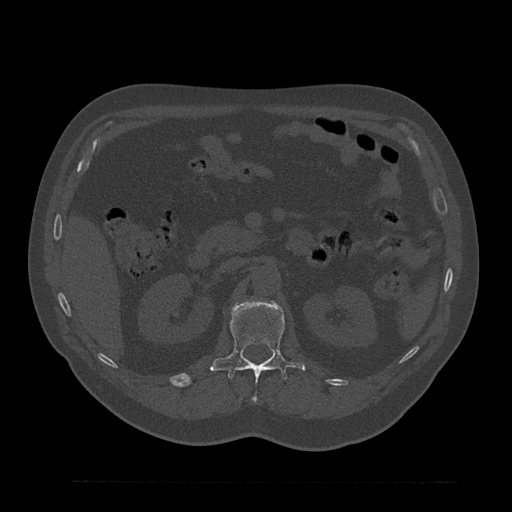
CT including the spine, one axial slice; position 166 of 797 along the scan axis; reconstruction kernel Br40s/3; bone window (W 1800 / L 400 HU); 0.5 mm slice thickness; 512 × 512 image matrix, field of view 430 × 430 mm. Patient: male, 61 years. Case-level facts recorded for this patient, not image findings: primary cancer: prostate.
Structures marked on this image (semi-automatically segmented with operator editing):
- L1 vertebra: bounding box [x1, y1, x2, y2] px = [210, 300, 305, 401]